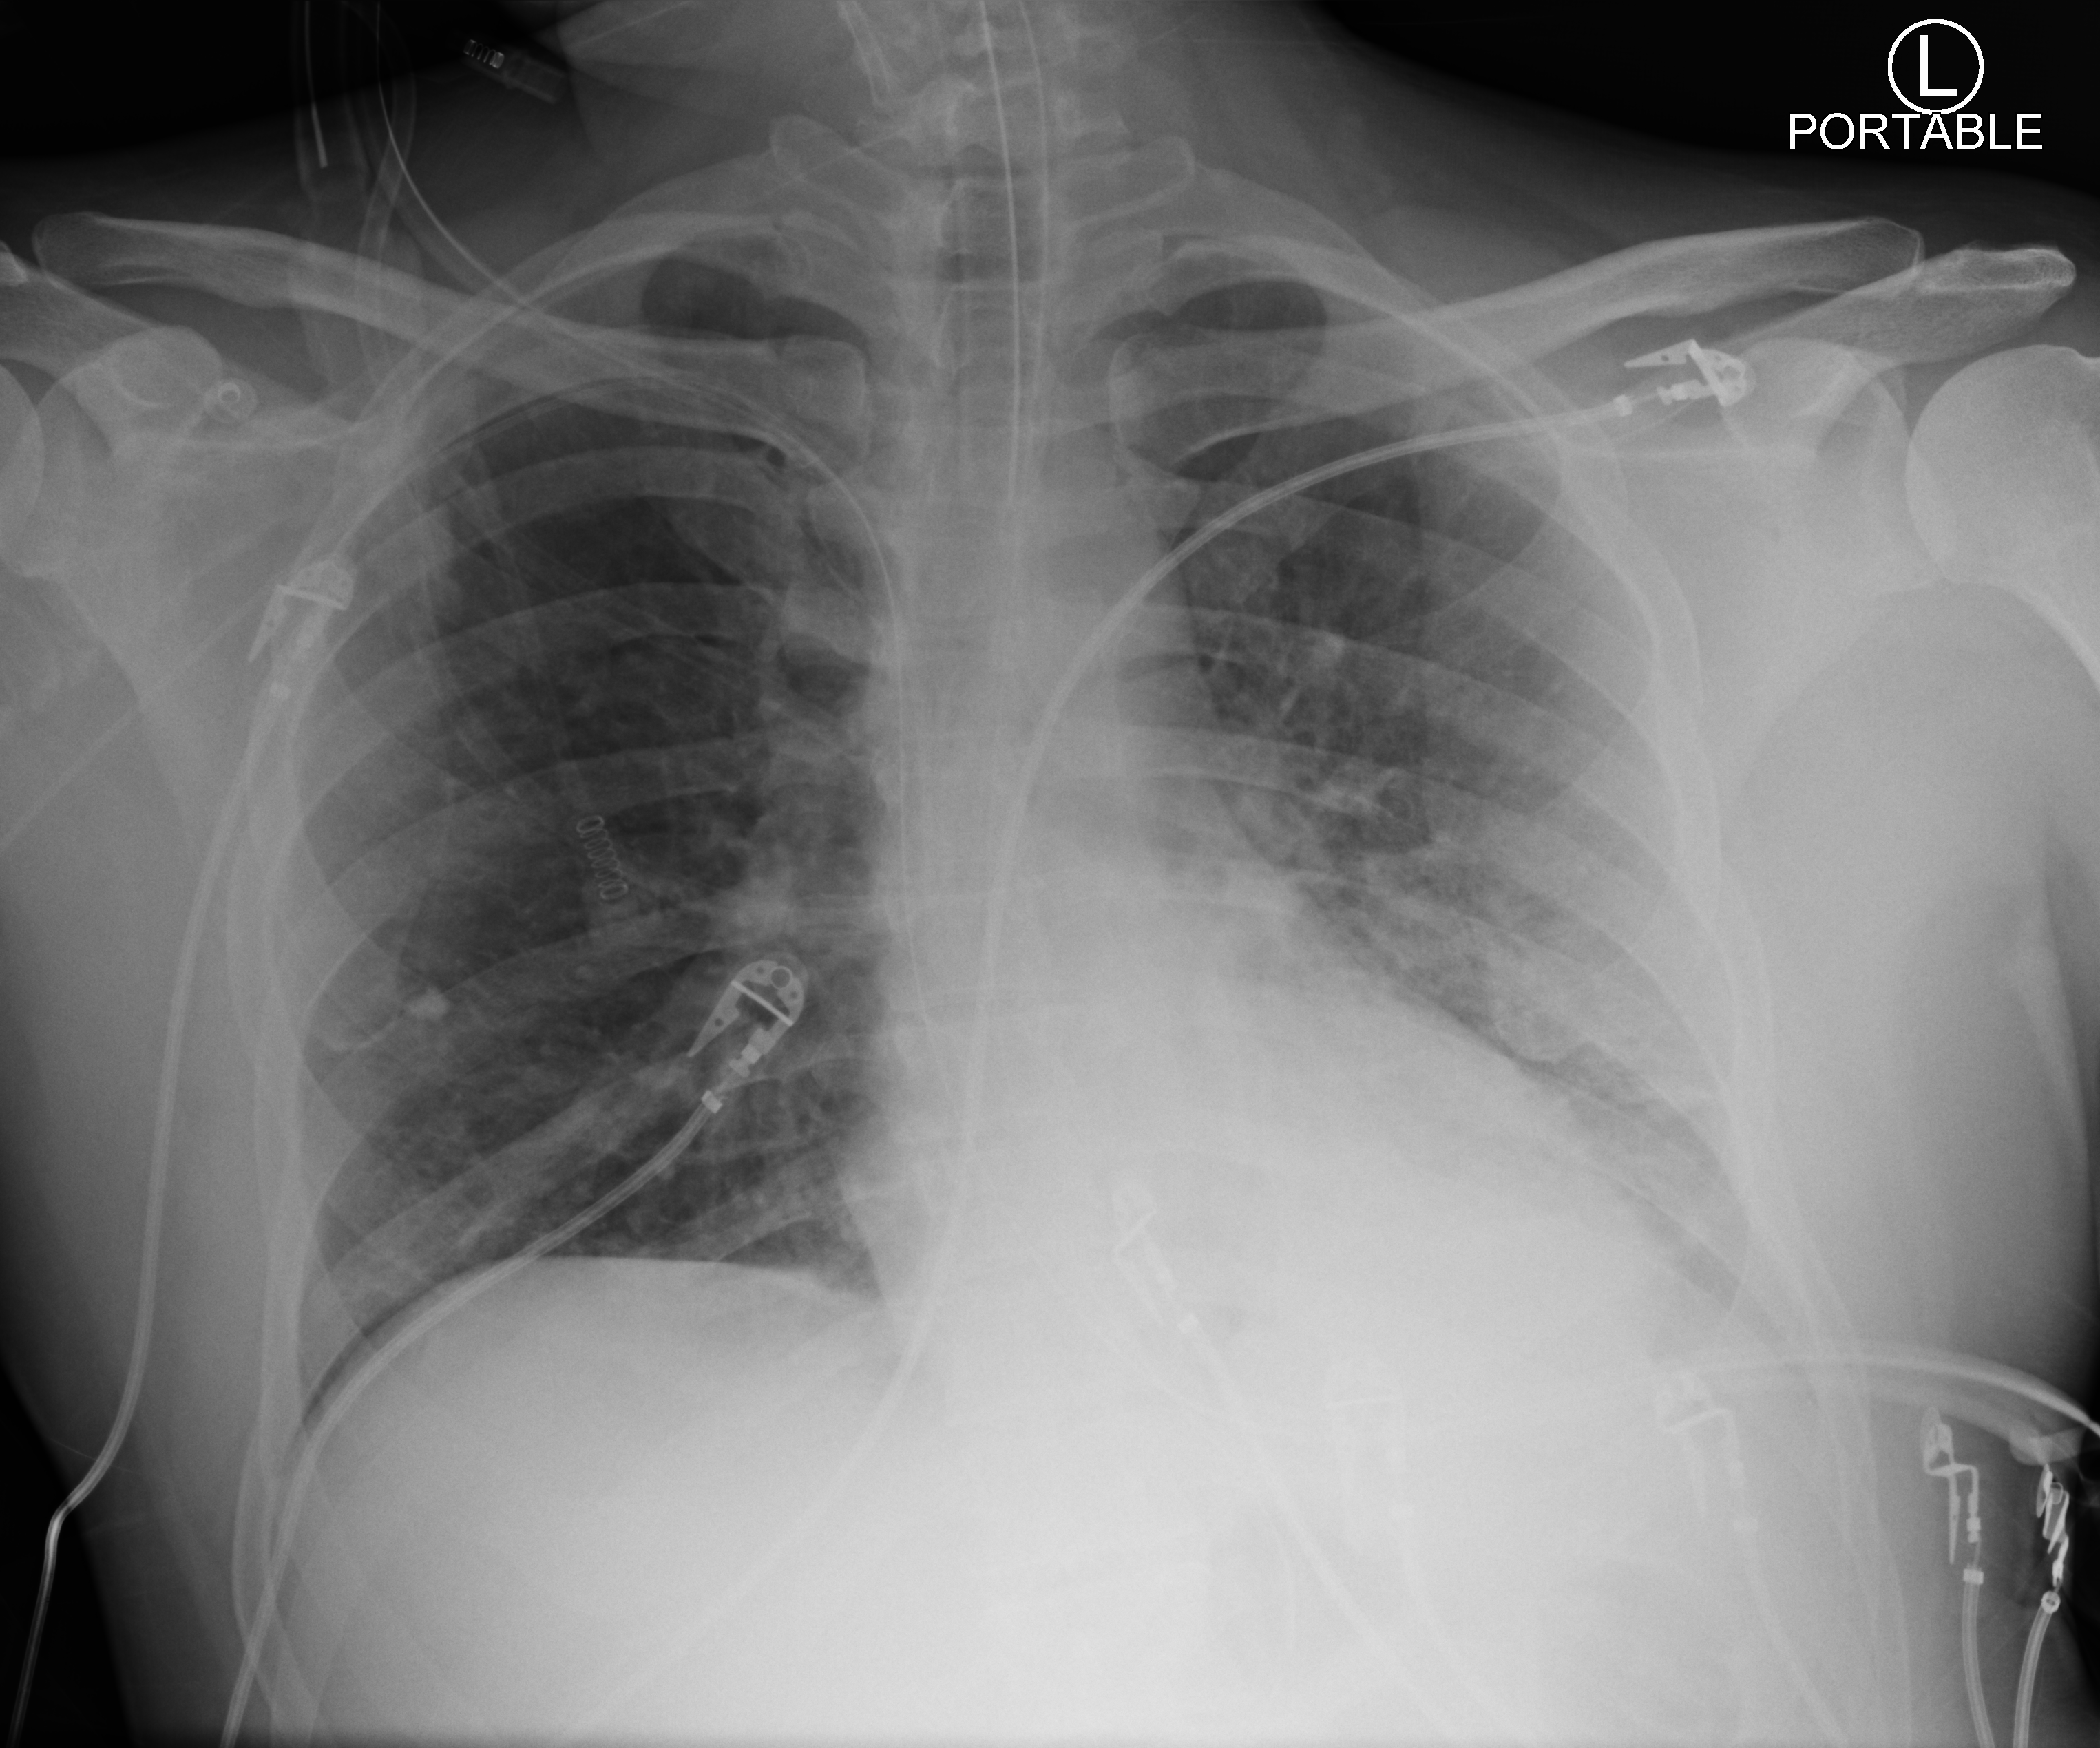
Portable chest radiograph, anteroposterior (AP) projection. Male patient hospitalised with COVID-19, age 18–59 years.
Admission-level facts for this patient (not findings on this image; timing relative to this image not recorded): smoking status (admission record): never.